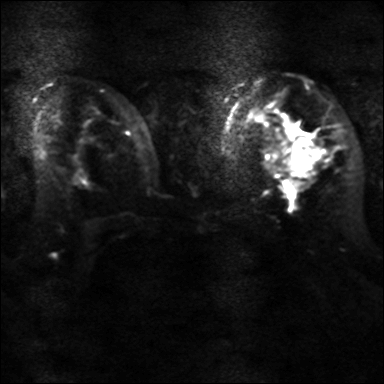
Breast MRI, one axial slice. Diffusion-weighted series; image 2 of 4 stored at this slice position (different b-values; order by instance number). 3 T. 384 × 384 image matrix, field of view 320 × 320 mm. Female patient.
Annotated regions visible in this slice (outlined manually by an expert reader):
- tumour on diffusion-weighted imaging: bounding box (x1, y1, x2, y2) in pixels: (284, 137, 321, 178)